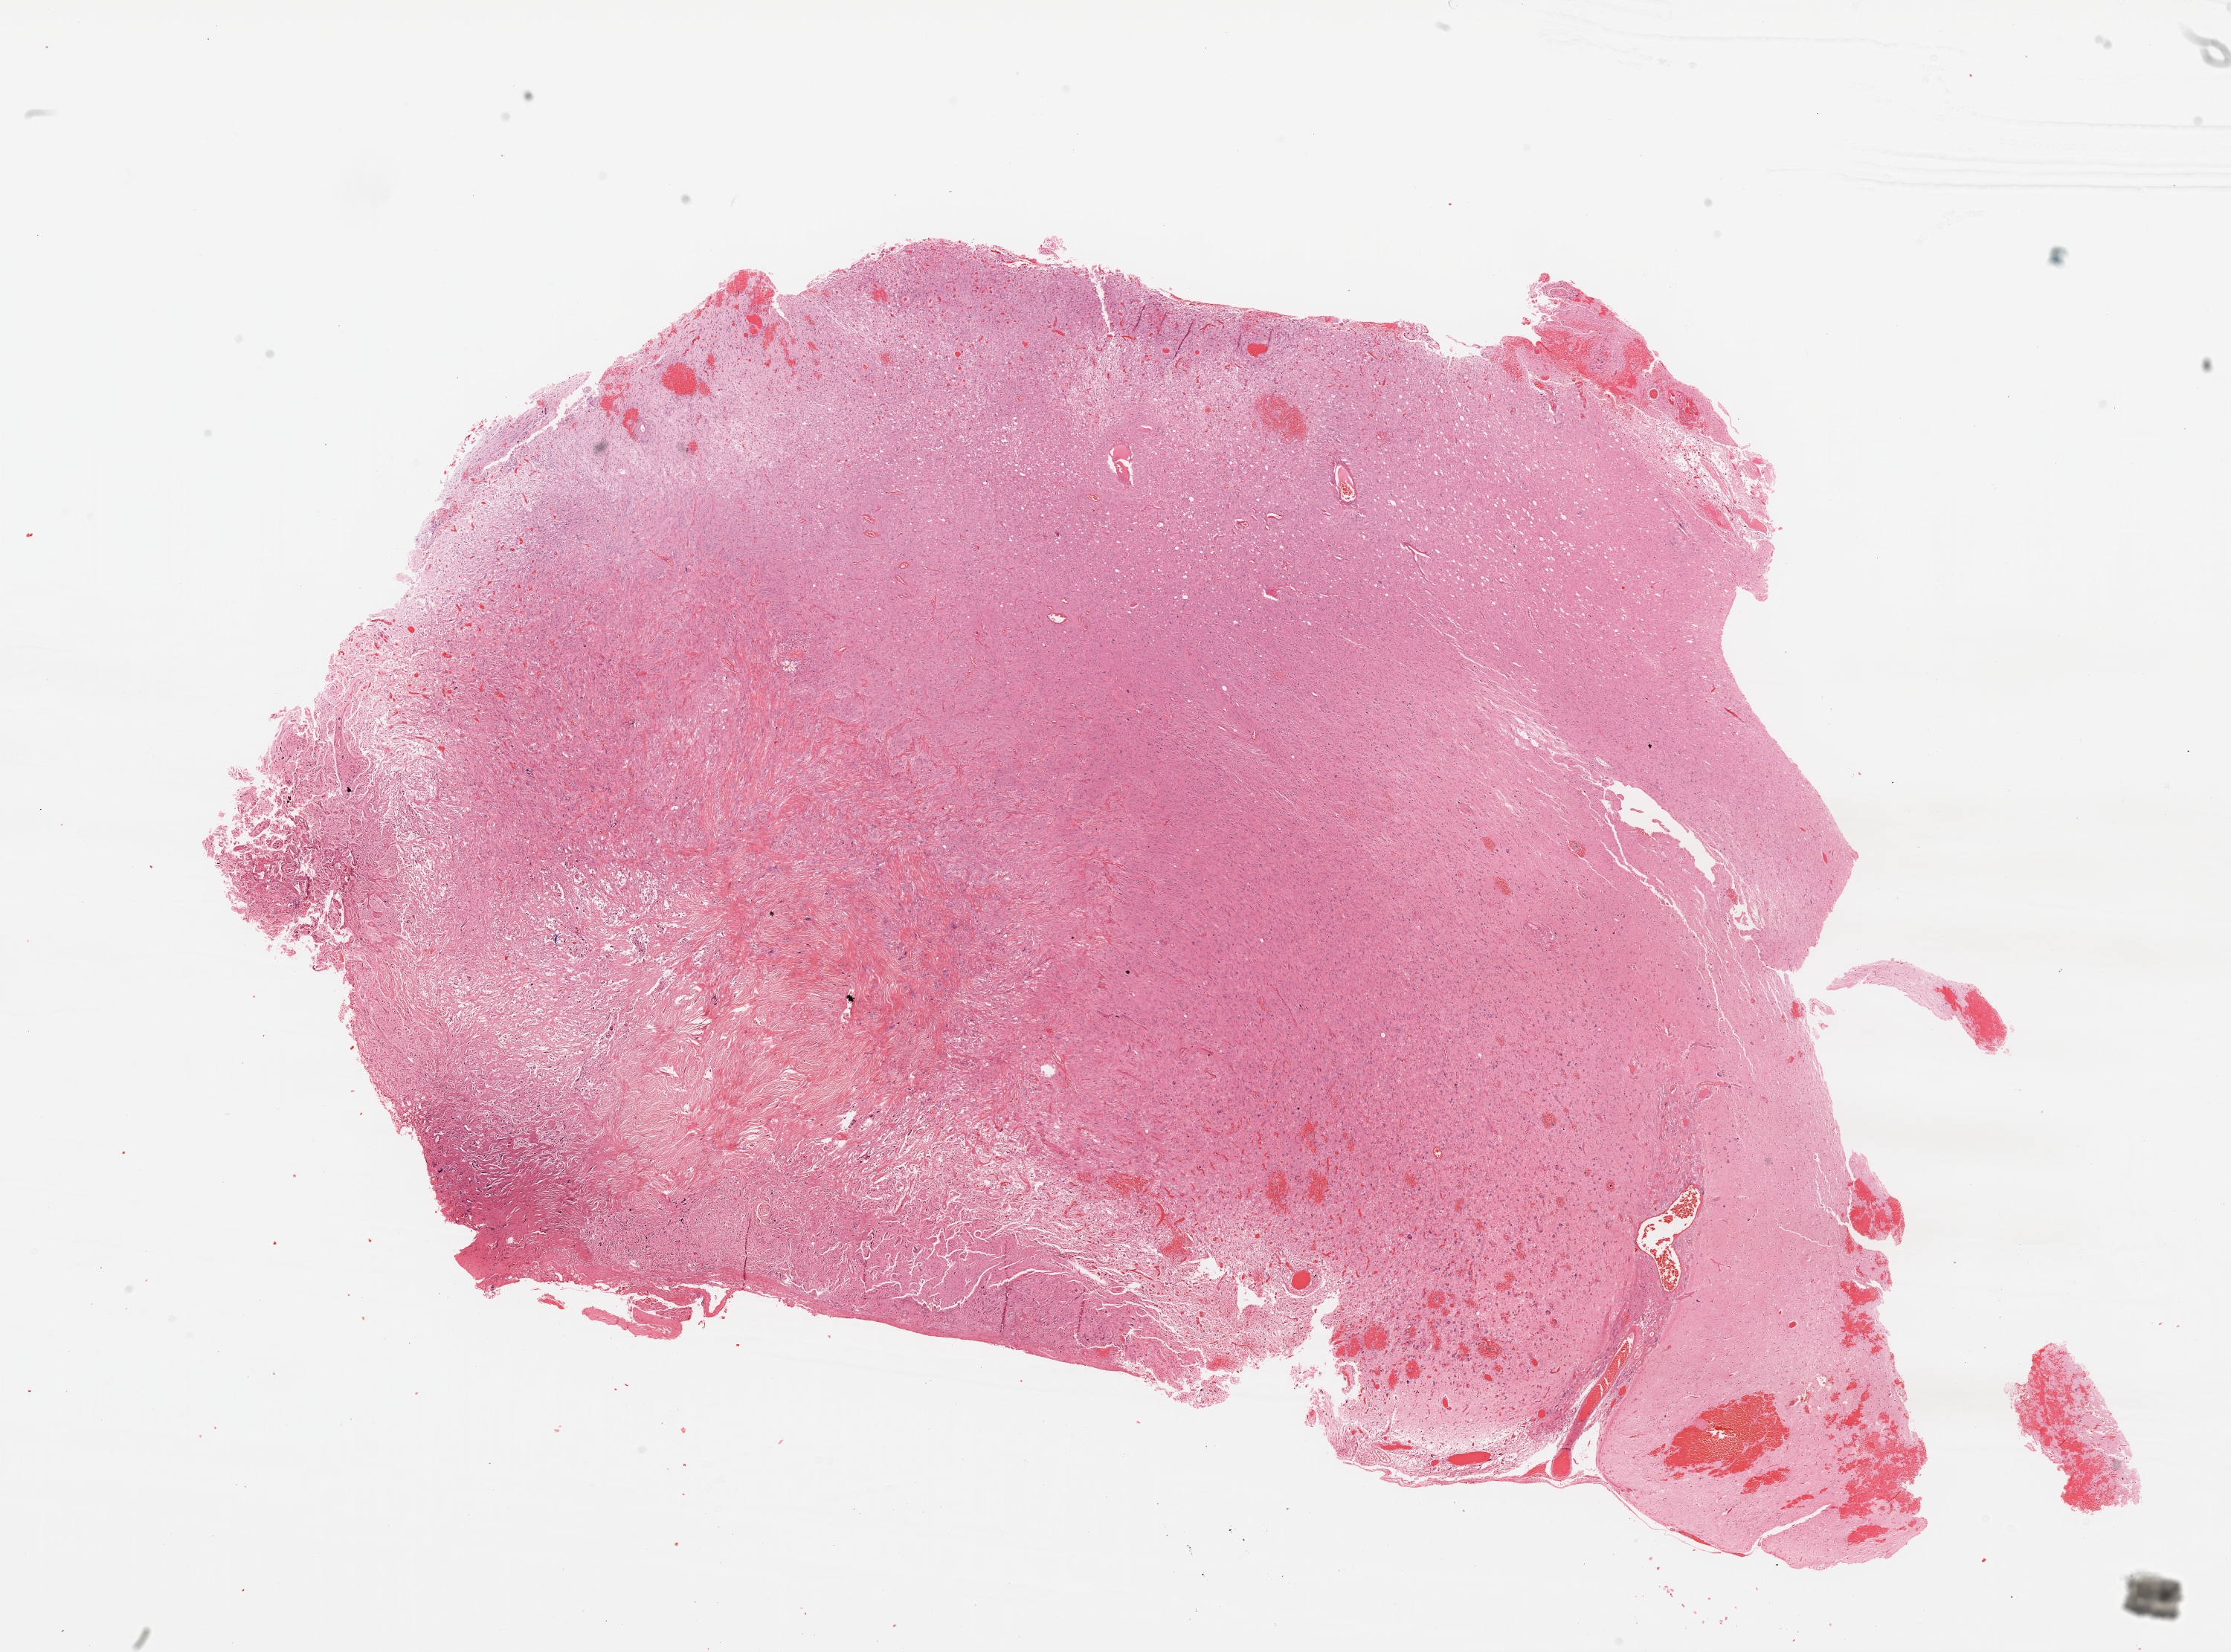
H&E-stained whole-slide image — shown as a low-resolution overview of the whole scanned area (about 24.1 x 17.8 mm, acquisition: 20x scan); formalin-fixed paraffin-embedded (FFPE) diagnostic section; primary tumour sample from the brain. Female patient; age at initial diagnosis 44 years.
• pathologic diagnosis: Glioblastoma